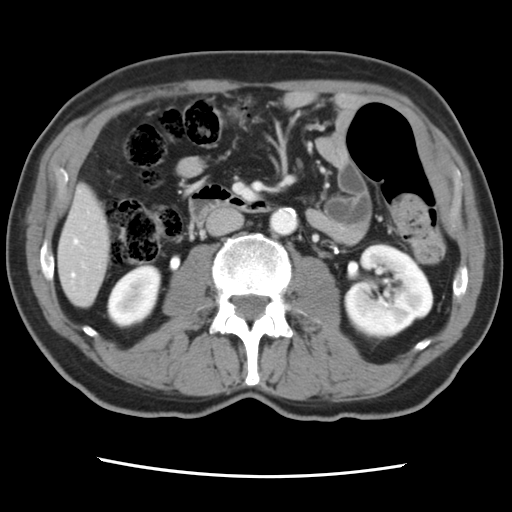
Contrast-enhanced abdominal CT, one axial slice; slice 23 of 83 in the series (ordered by position); 120 kVp; intravenous contrast given; soft-tissue window (W 400 / L 40 HU); 5 mm slice thickness; 512 × 512 image matrix, field of view 321 × 321 mm. Male patient, age 69 years. From the clinical record (not read from this slice): diagnosis: colorectal cancer liver metastases, imaged before liver resection; multiple liver metastases: yes; largest metastasis: 3.5 cm; disease in both lobes: no.
Outlined on this slice (expert manual segmentation):
- hepatic veins: bounding box <72,239,78,276> (left, top, right, bottom; pixels)
- liver: <59,188,110,305>
- planned liver remnant (the part of the liver to remain after resection): <59,188,110,306>